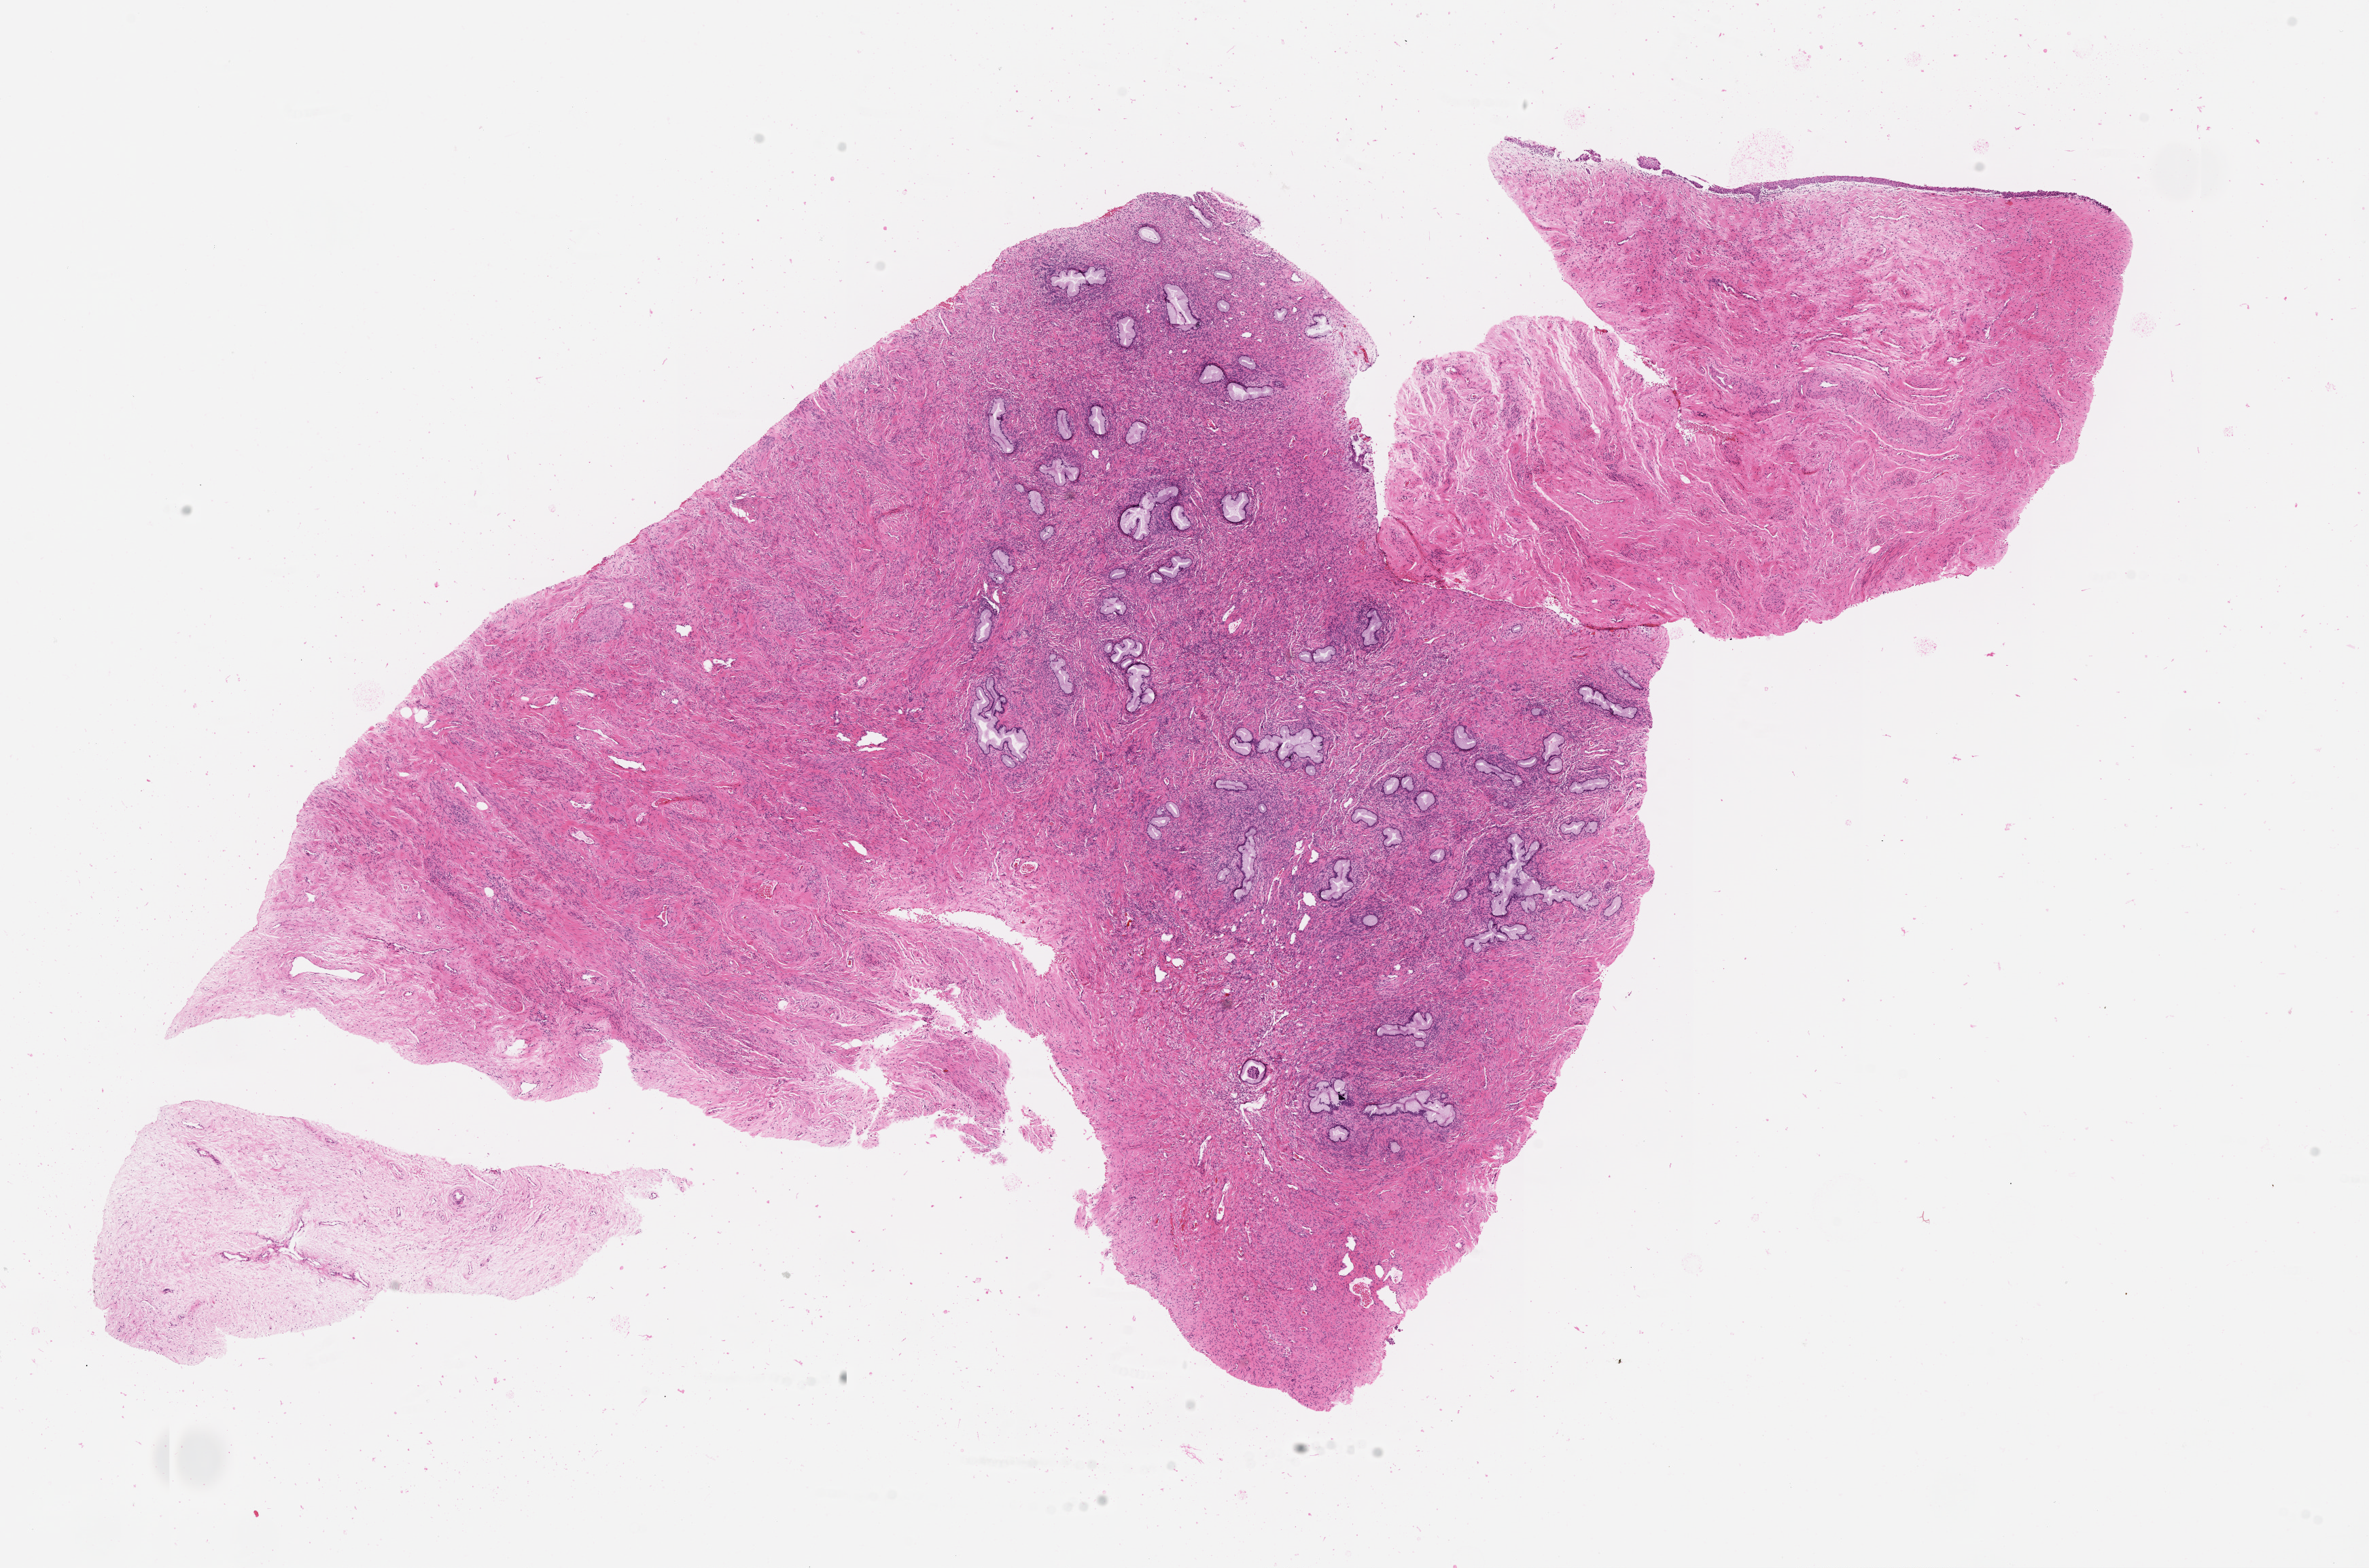
Digitized Hematoxylin and eosin (H&E) stained tissue section (whole slide) — low-resolution overview of the scanned area, about 14.0 x 9.3 mm (slide scanned at 20x), normal (non-tumour) tissue sample, uterus. 70-year-old female patient.
• this section: normal (non-tumour) tissue from the same patient
• patient diagnosis: Endometrioid adenocarcinoma, NOS